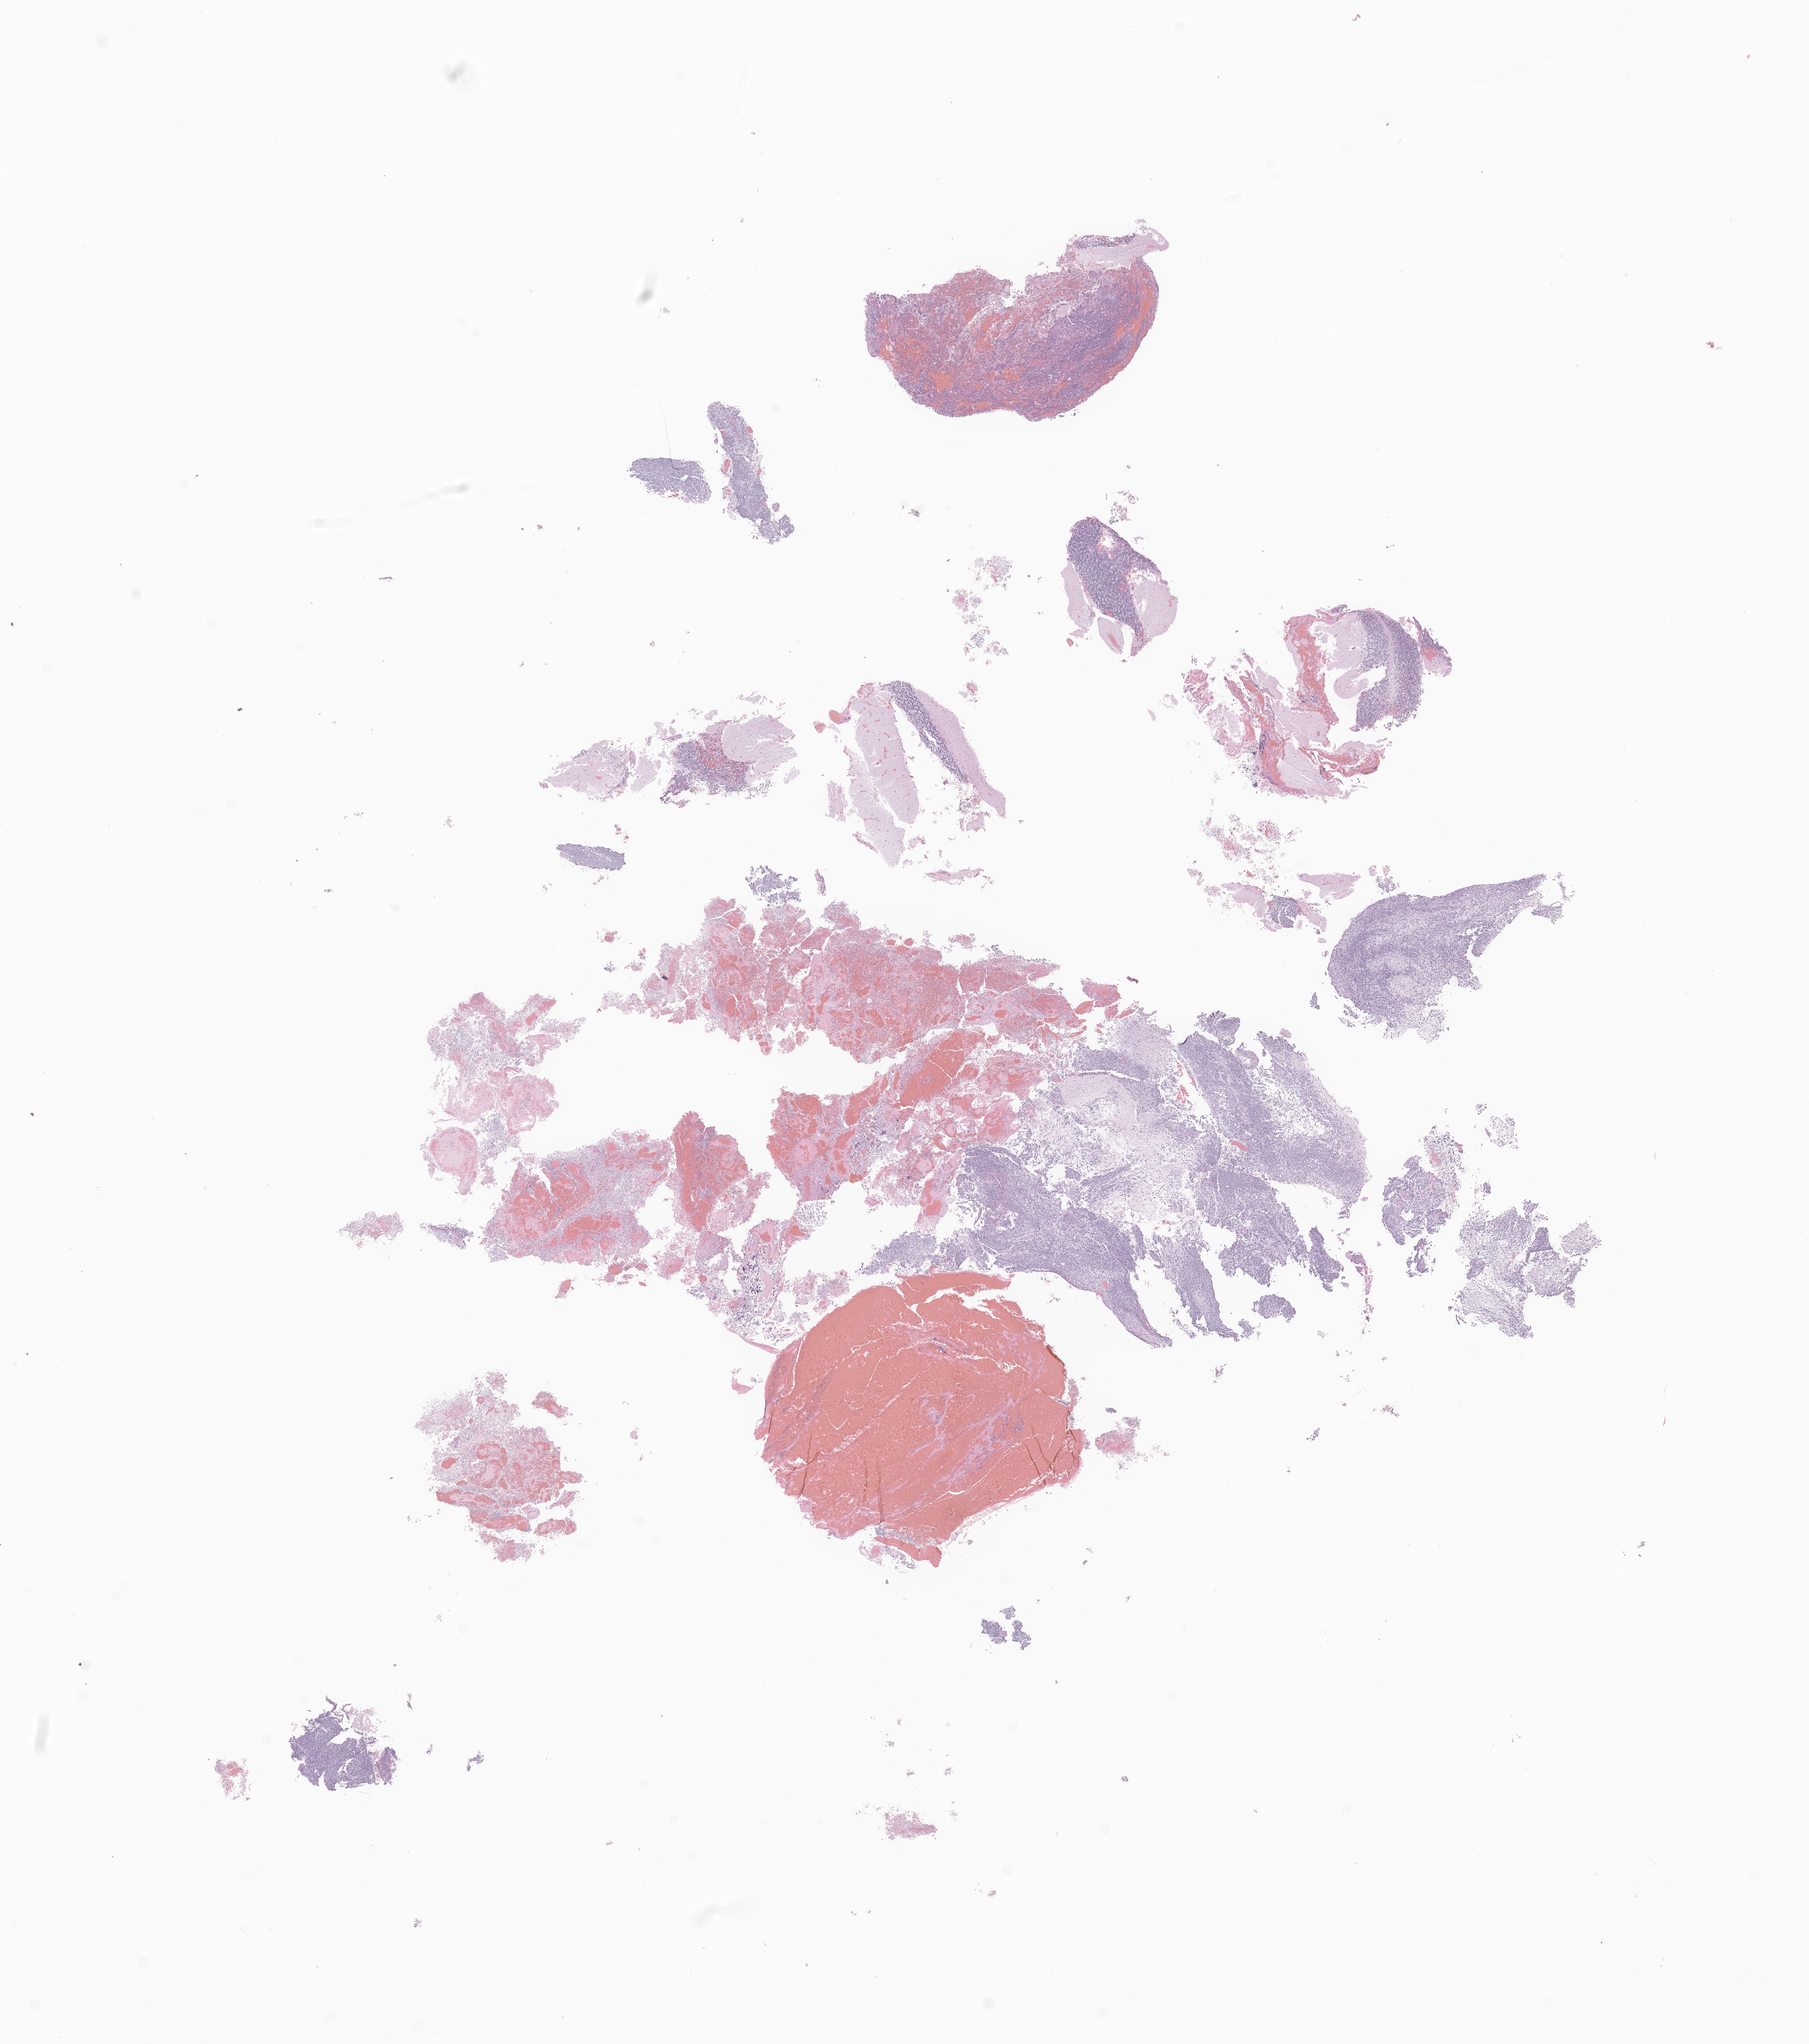
Digitized hematoxylin and eosin (H&E)-stained section of tumor tissue from the brain — low-resolution overview of the scanned area, about 16.9 x 19.1 mm, FFPE section. Female patient, age 314 days.
Diagnosis (ICD-O-3 morphology term): Atypical teratoid/rhabdoid tumor.